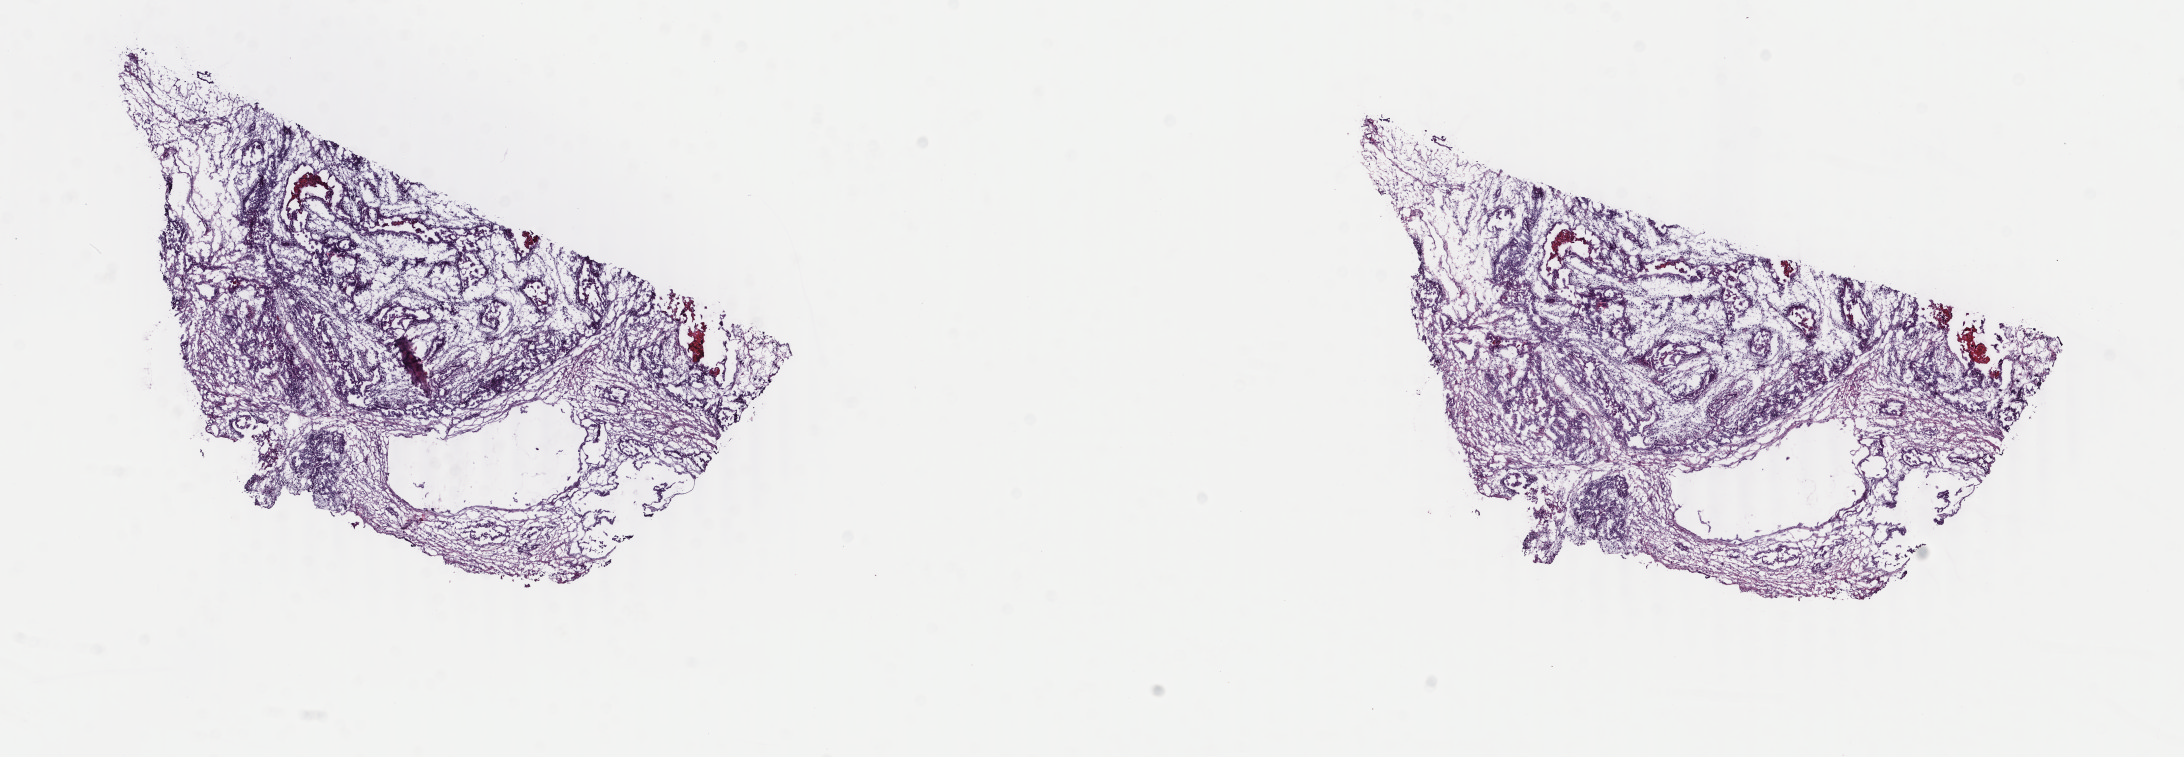
Whole-slide histology image, H&E, shown as a low-resolution overview of the whole scanned area (about 17.4 x 6.0 mm, slide scanned at 40x). Frozen section from the top of the tissue portion. Primary tumour sample from the uterus. Female, age 61 years at initial diagnosis. Slide review estimates, as recorded: tumour cells 60%, tumour nuclei 90%, normal cells 0%, stromal cells 20%, necrosis 20%. Inflammatory infiltration, as recorded: lymphocyte infiltration 0%, monocyte infiltration 0%, neutrophil infiltration 0%.
Lymph nodes positive (case pathology): 3 of 3 examined. FIGO stage: IVB. Diagnosis: Mullerian mixed tumor.